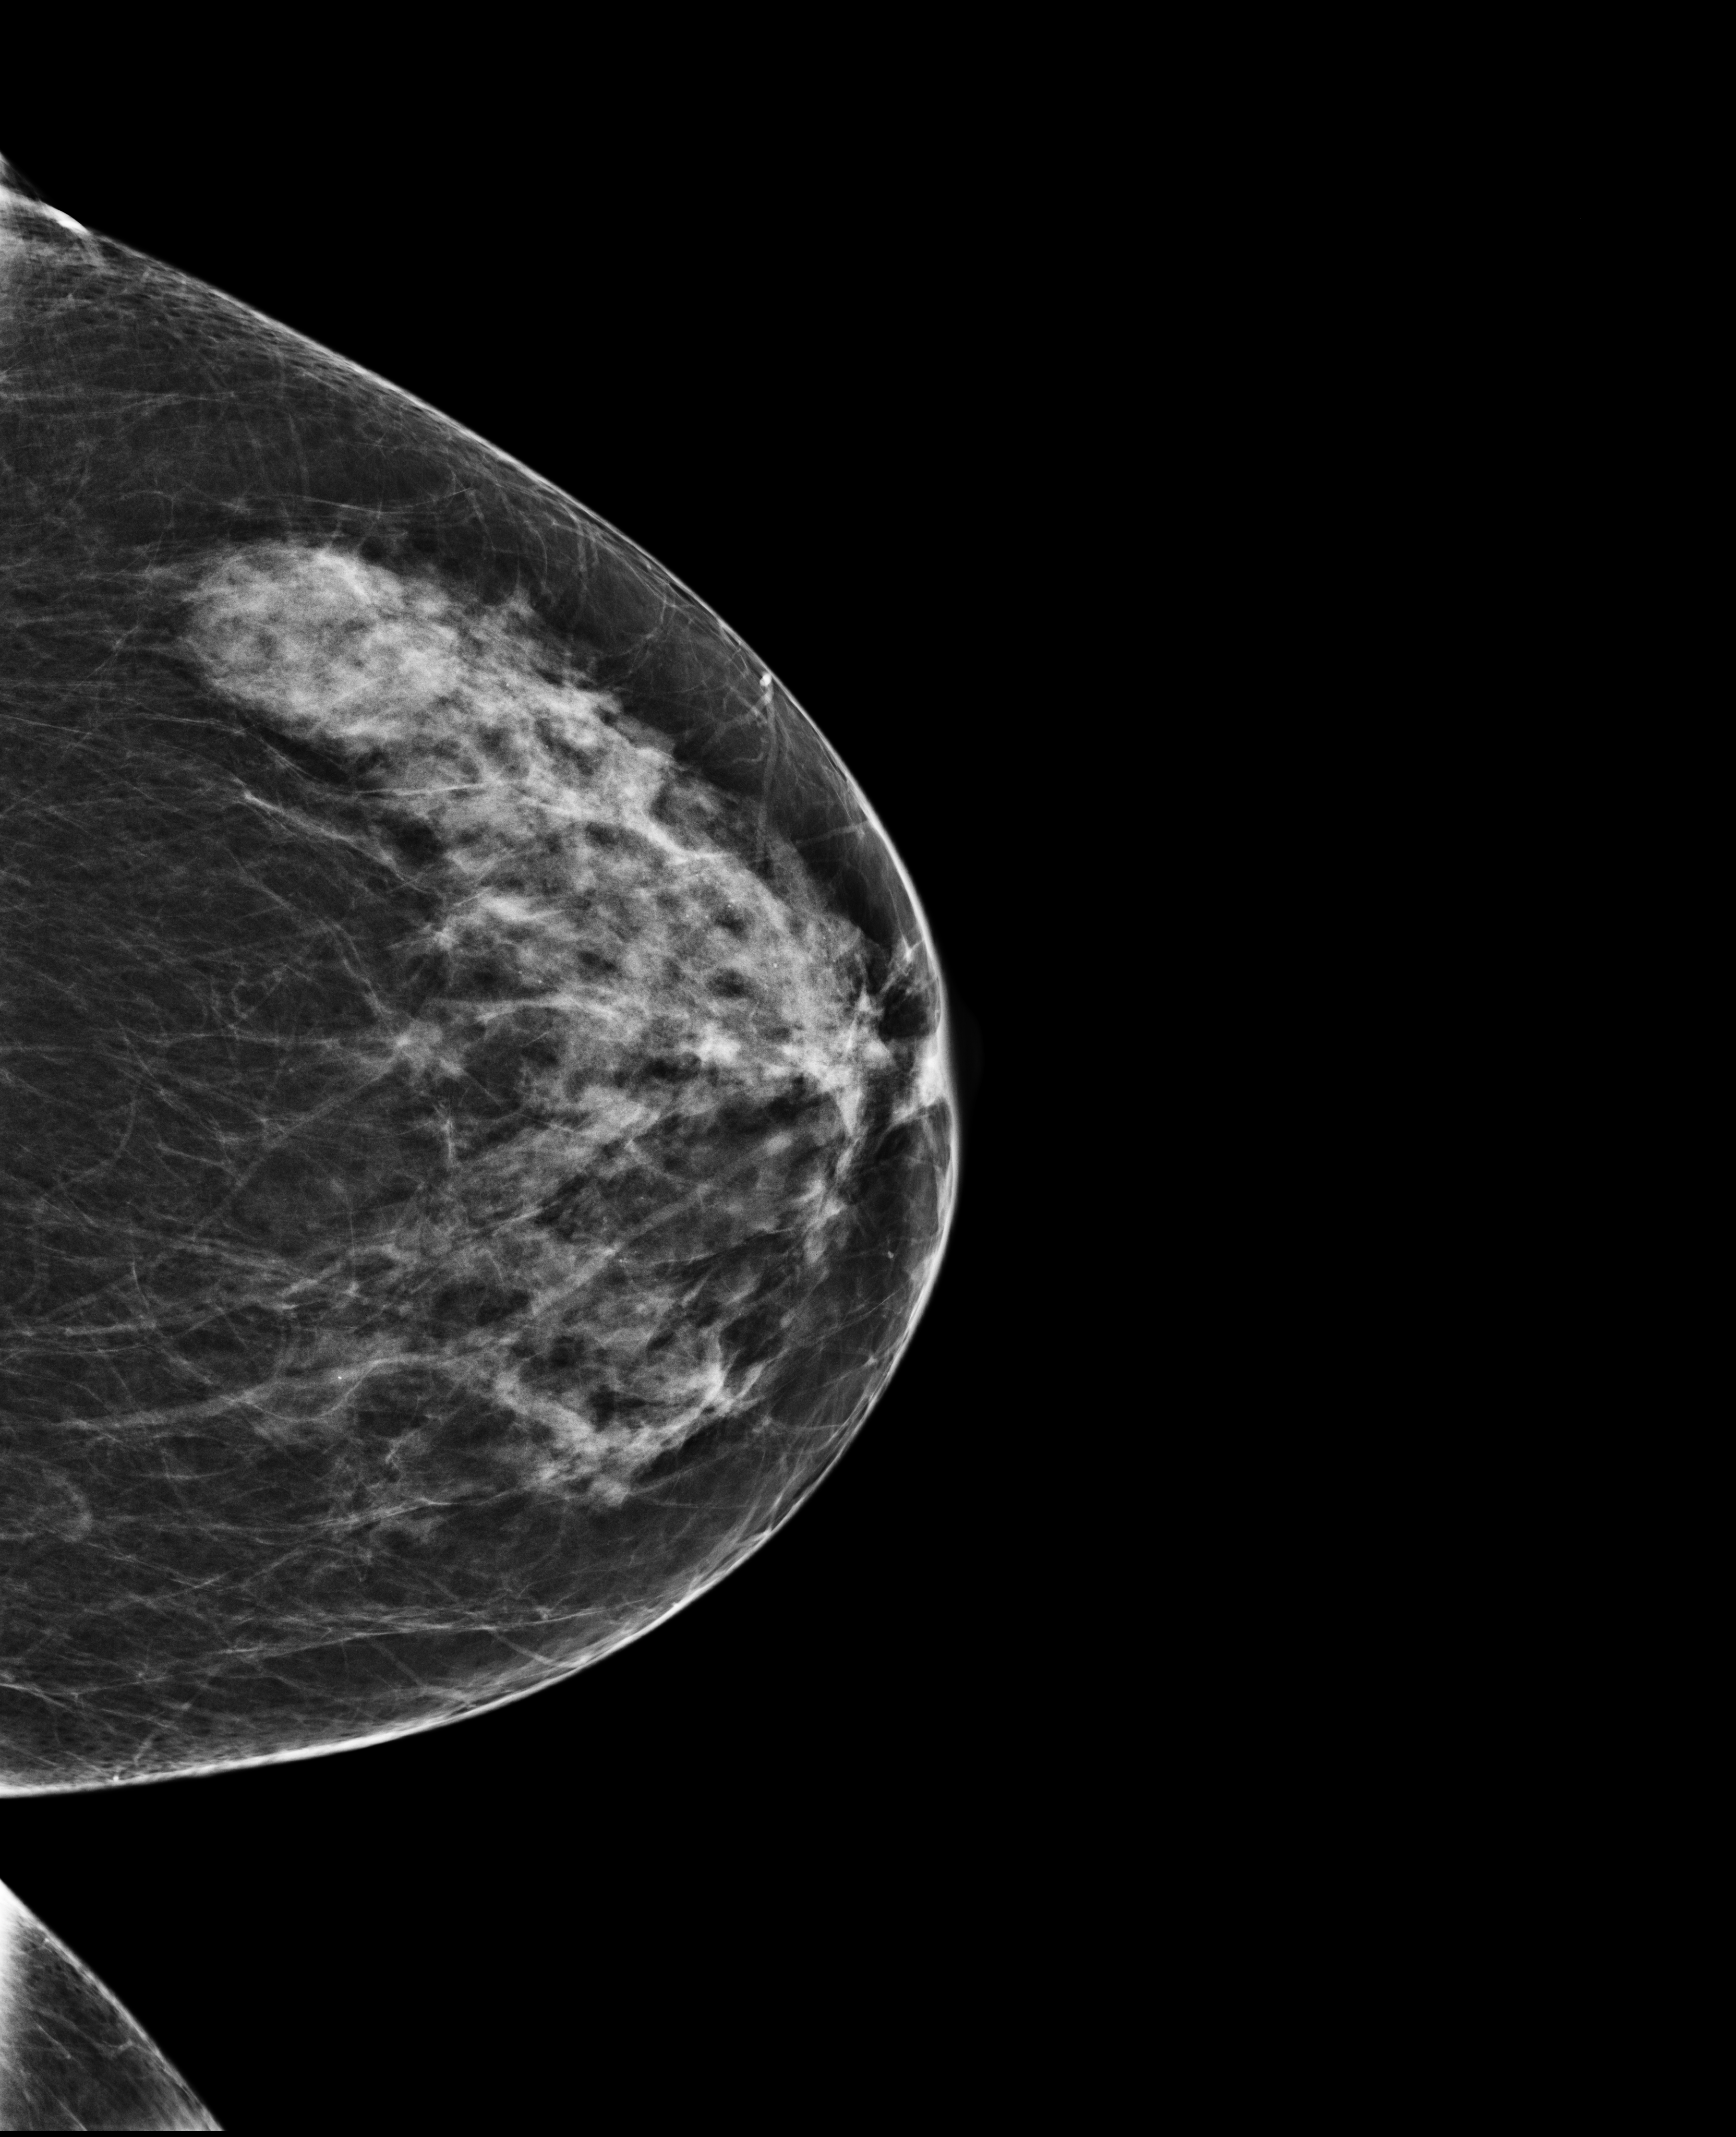
Annual screening mammography examination, system: Selenia Dimensions. Female patient, age 49 years.
Image type: full-field digital mammogram. Breast: left. Projection: cranio-caudal projection.